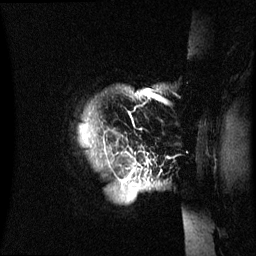
Breast MRI (dynamic contrast-enhanced), one sagittal slice; position 58 of 60 along the scan axis; dynamic contrast-enhanced series, image 2 of 3 at this slice position (ordered by acquisition); 1.5 T; TE 4.2 ms, TR 8.4 ms; 2.4 mm slice thickness; 256 × 256 image matrix. Patient: female, 48 years.
Outlined on this slice (semi-automatic segmentation, software-assisted and operator-edited):
- analysis volume of interest (the breast-tissue region the enhancement analysis was run in; not a lesion): bounding box (x1, y1, x2, y2) in pixels: (80, 88, 189, 231)
- tumour enhancement mask (voxels above the 70 % enhancement threshold inside the analysis volume of interest): (122, 92, 142, 183)